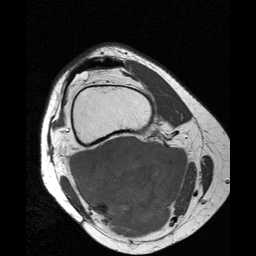
MRI of an extremity soft-tissue mass, one axial slice; slice 17 of 25 in the series (ordered by position); 256 × 256 image matrix. Female patient. Case-level facts recorded for this patient, not image findings: histological type: liposarcoma; site of the primary tumour: right thigh.
Structures marked on this image (outlined manually by an expert reader):
- gross tumour volume (mass): bounding box [x1, y1, x2, y2] px = [69, 136, 189, 239]